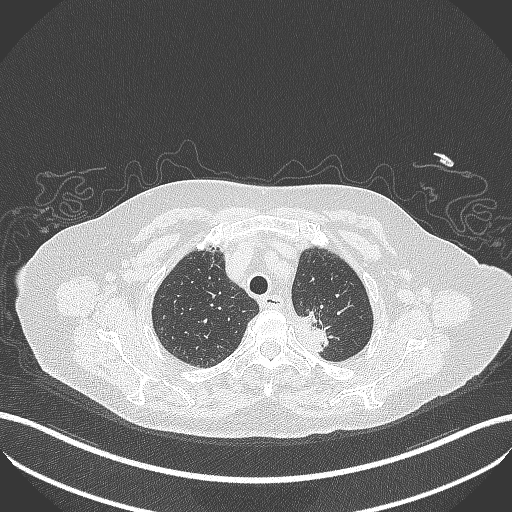
Chest CT, one axial slice; slice 283 of 353 in the series (ordered by position); reconstruction kernel B70f; lung window (W 1500 / L -600 HU); 1 mm slice thickness; 512 × 512 image matrix, field of view 400 × 400 mm. Patient: female, 81 years. Case-level facts recorded for this patient, not image findings: clinical TNM (as recorded): T2a N0 M0.
Outlined on this slice (bounding box drawn by a radiologist):
- lung tumour (recorded histology: adenocarcinoma): box from (x=287, y=305) to (x=334, y=354) px